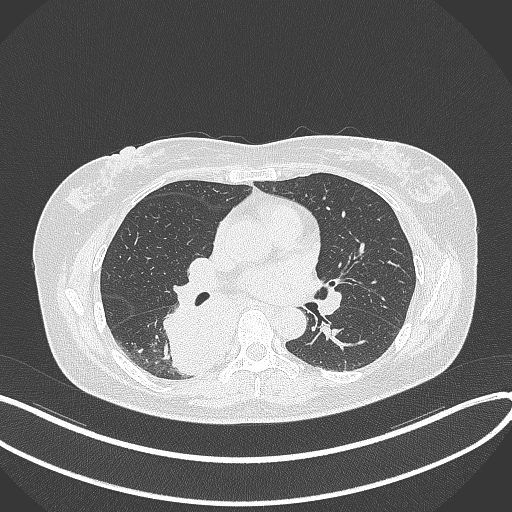
Chest CT, one axial slice. Slice 193 of 331 in the series (ordered by position). Reconstruction kernel B70f. 120 kVp. Lung window (W 1500 / L -600 HU). 1 mm slice thickness. 512 × 512 image matrix. Female patient, age 54 years. From the clinical record (not read from this slice): clinical TNM (as recorded): T4 N0 M0.
Annotated regions visible in this slice (rectangle marked by the reading radiologist):
- lung tumour (recorded histology: adenocarcinoma): bounding box [x1, y1, x2, y2] px = [165, 293, 236, 378]